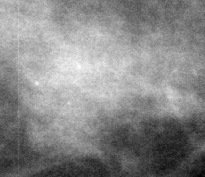
Region of interest cut from a scanned film mammogram (one marked finding), left breast, MLO view, BI-RADS breast density category 1 (scale 1–4).
Marked abnormality: mass, shape oval, margins microlobulated; BI-RADS assessment category 4; pathology result (as recorded, not read from the image): malignant.